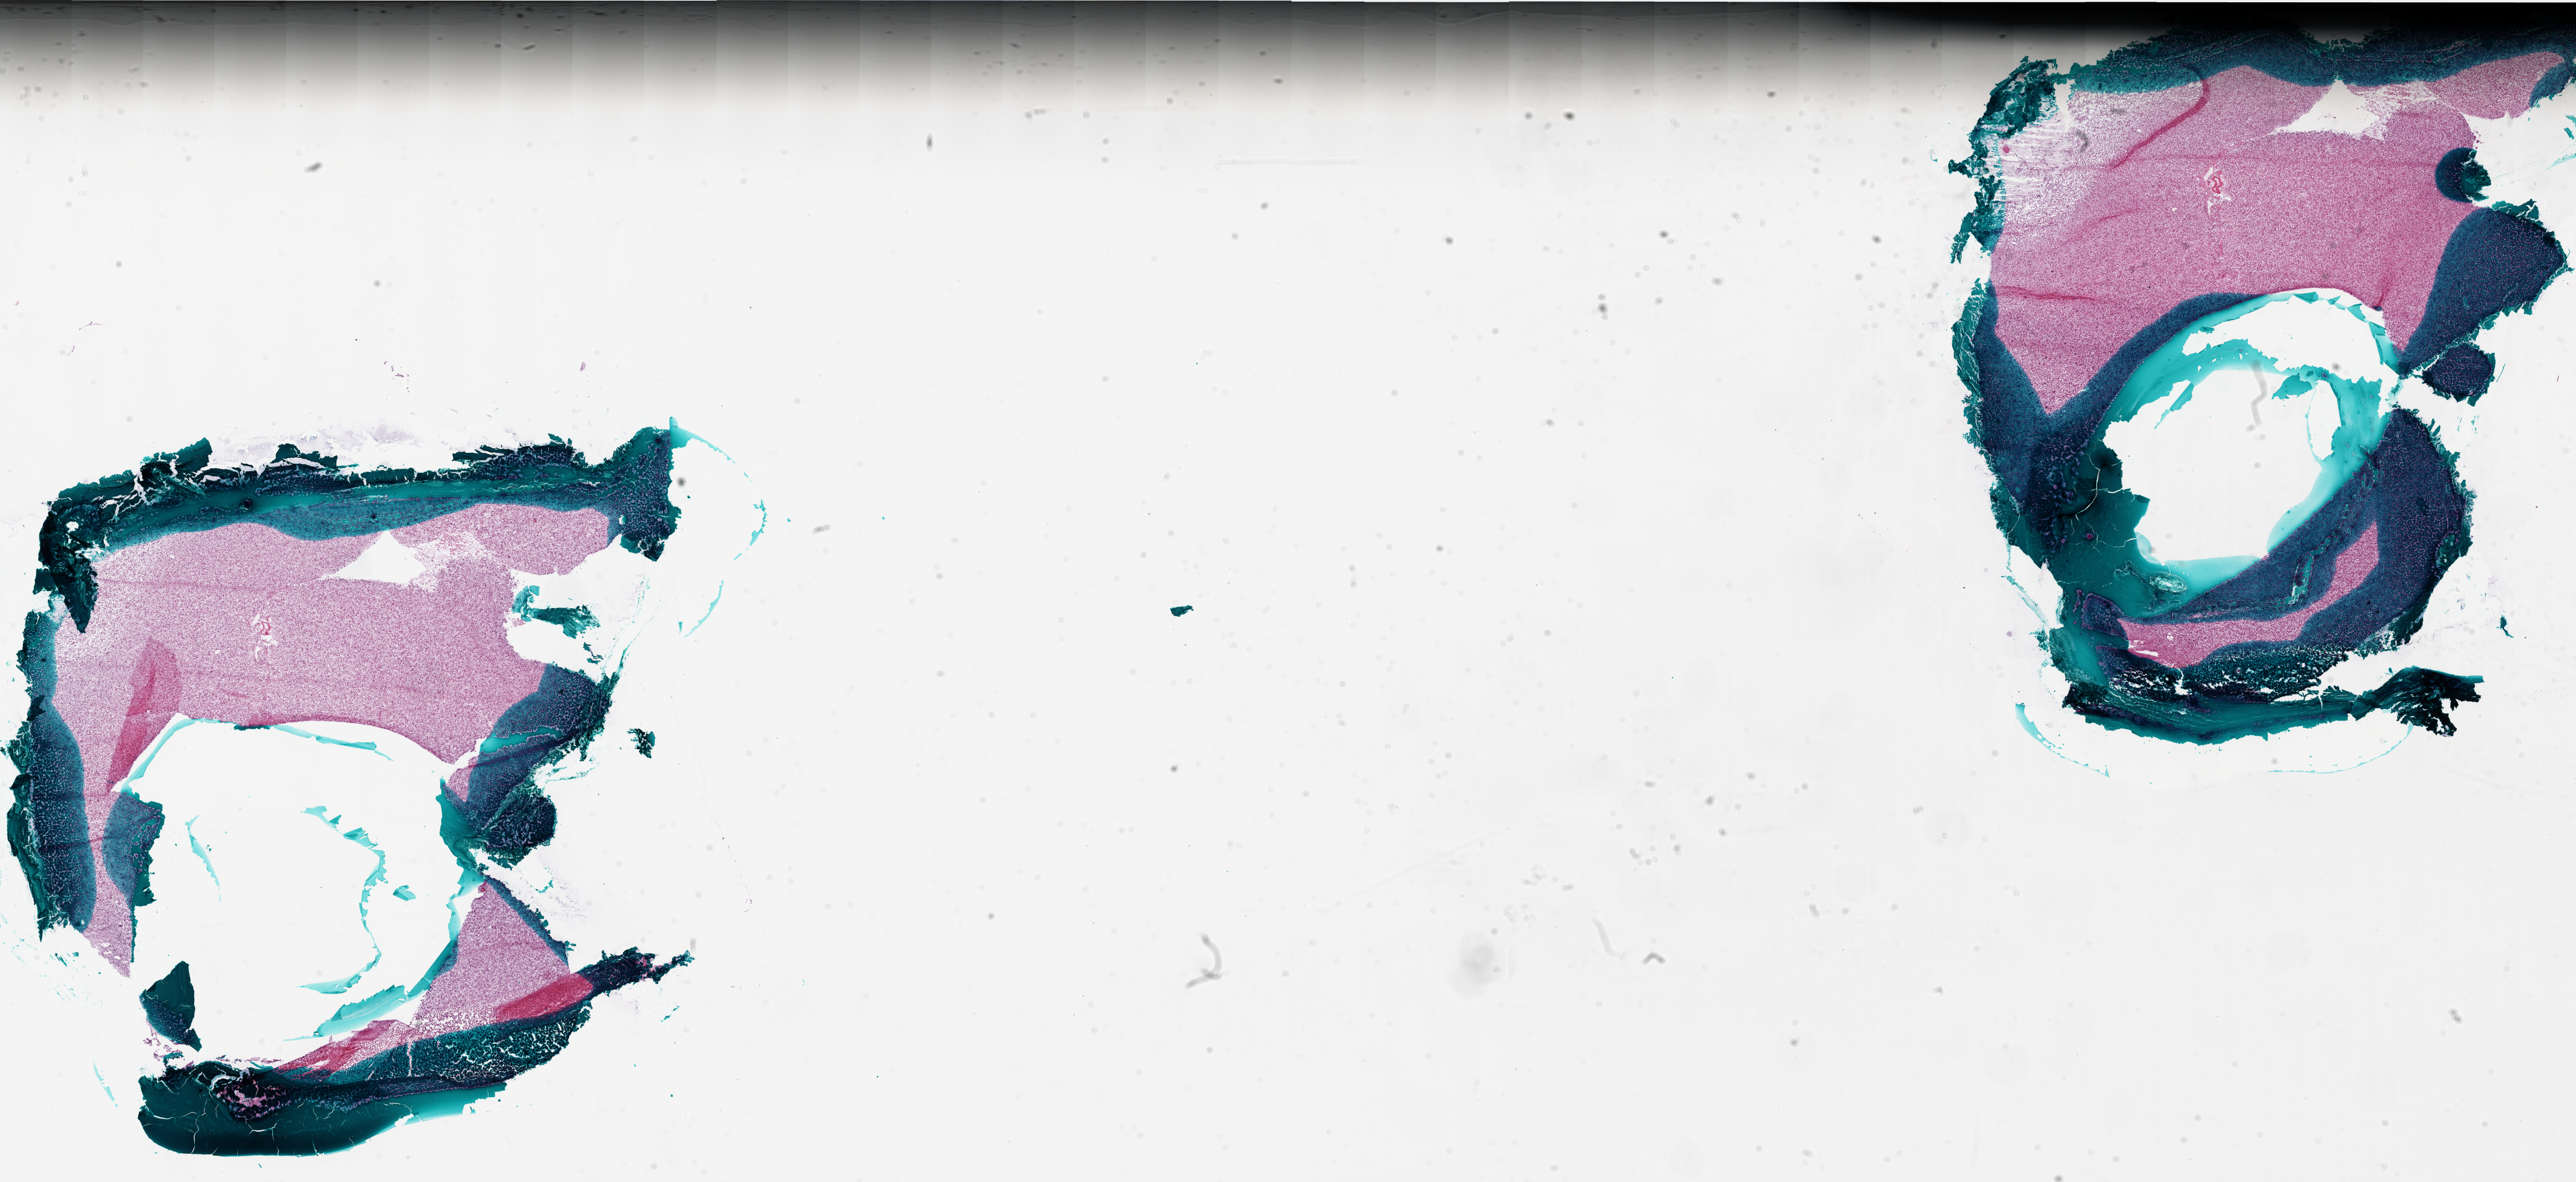
Digitized H&E-stained tissue section (whole slide) — whole scanned area (about 36.0 x 16.5 mm, acquisition: 20x scan) shown as a low-resolution overview; frozen section from the bottom of the tissue portion; sample: primary tumour, brain. Male patient; age at initial diagnosis 80 years. Pathologist review of this section (percent, as recorded): tumour cells 90%, tumour nuclei 100%, normal cells 0%, stromal cells 0%, necrosis 10%.
• diagnosis: Glioblastoma